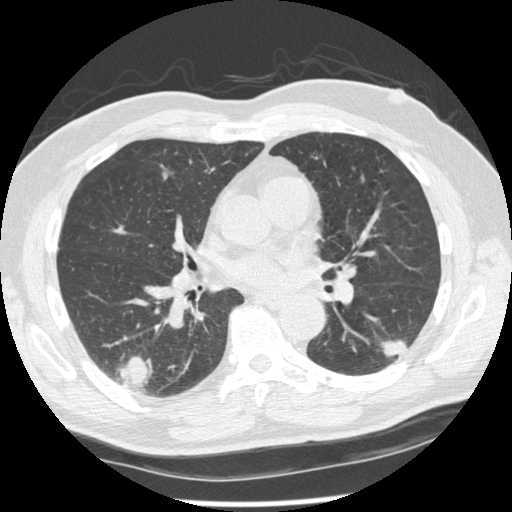
Chest CT (low-dose screening protocol), one axial image. Second annual screen. Lung window (W 1500 / L -600 HU). 1.25 mm slice thickness. Standard (soft-tissue) reconstruction kernel (STANDARD). 120 kVp. Slice 122 of 227 in the series. Male participant, aged 74 years at enrolment.
Lesion marked by an expert reader, bounding box <367,313,424,368> (left, top, right, bottom; pixels). The screening reader recorded 7 non-calcified nodules or masses ≥4 mm on this exam (right upper lobe, right lower lobe, right upper lobe, right lower lobe, left lower lobe, left upper lobe, left upper lobe); which of them this box marks is not recorded. Participant outcome: lung cancer diagnosed 43 days after this screen — squamous cell carcinoma, NOS, left lower lobe, well differentiated (G1), stage IA (AJCC 6th edition), 28 mm at pathology.